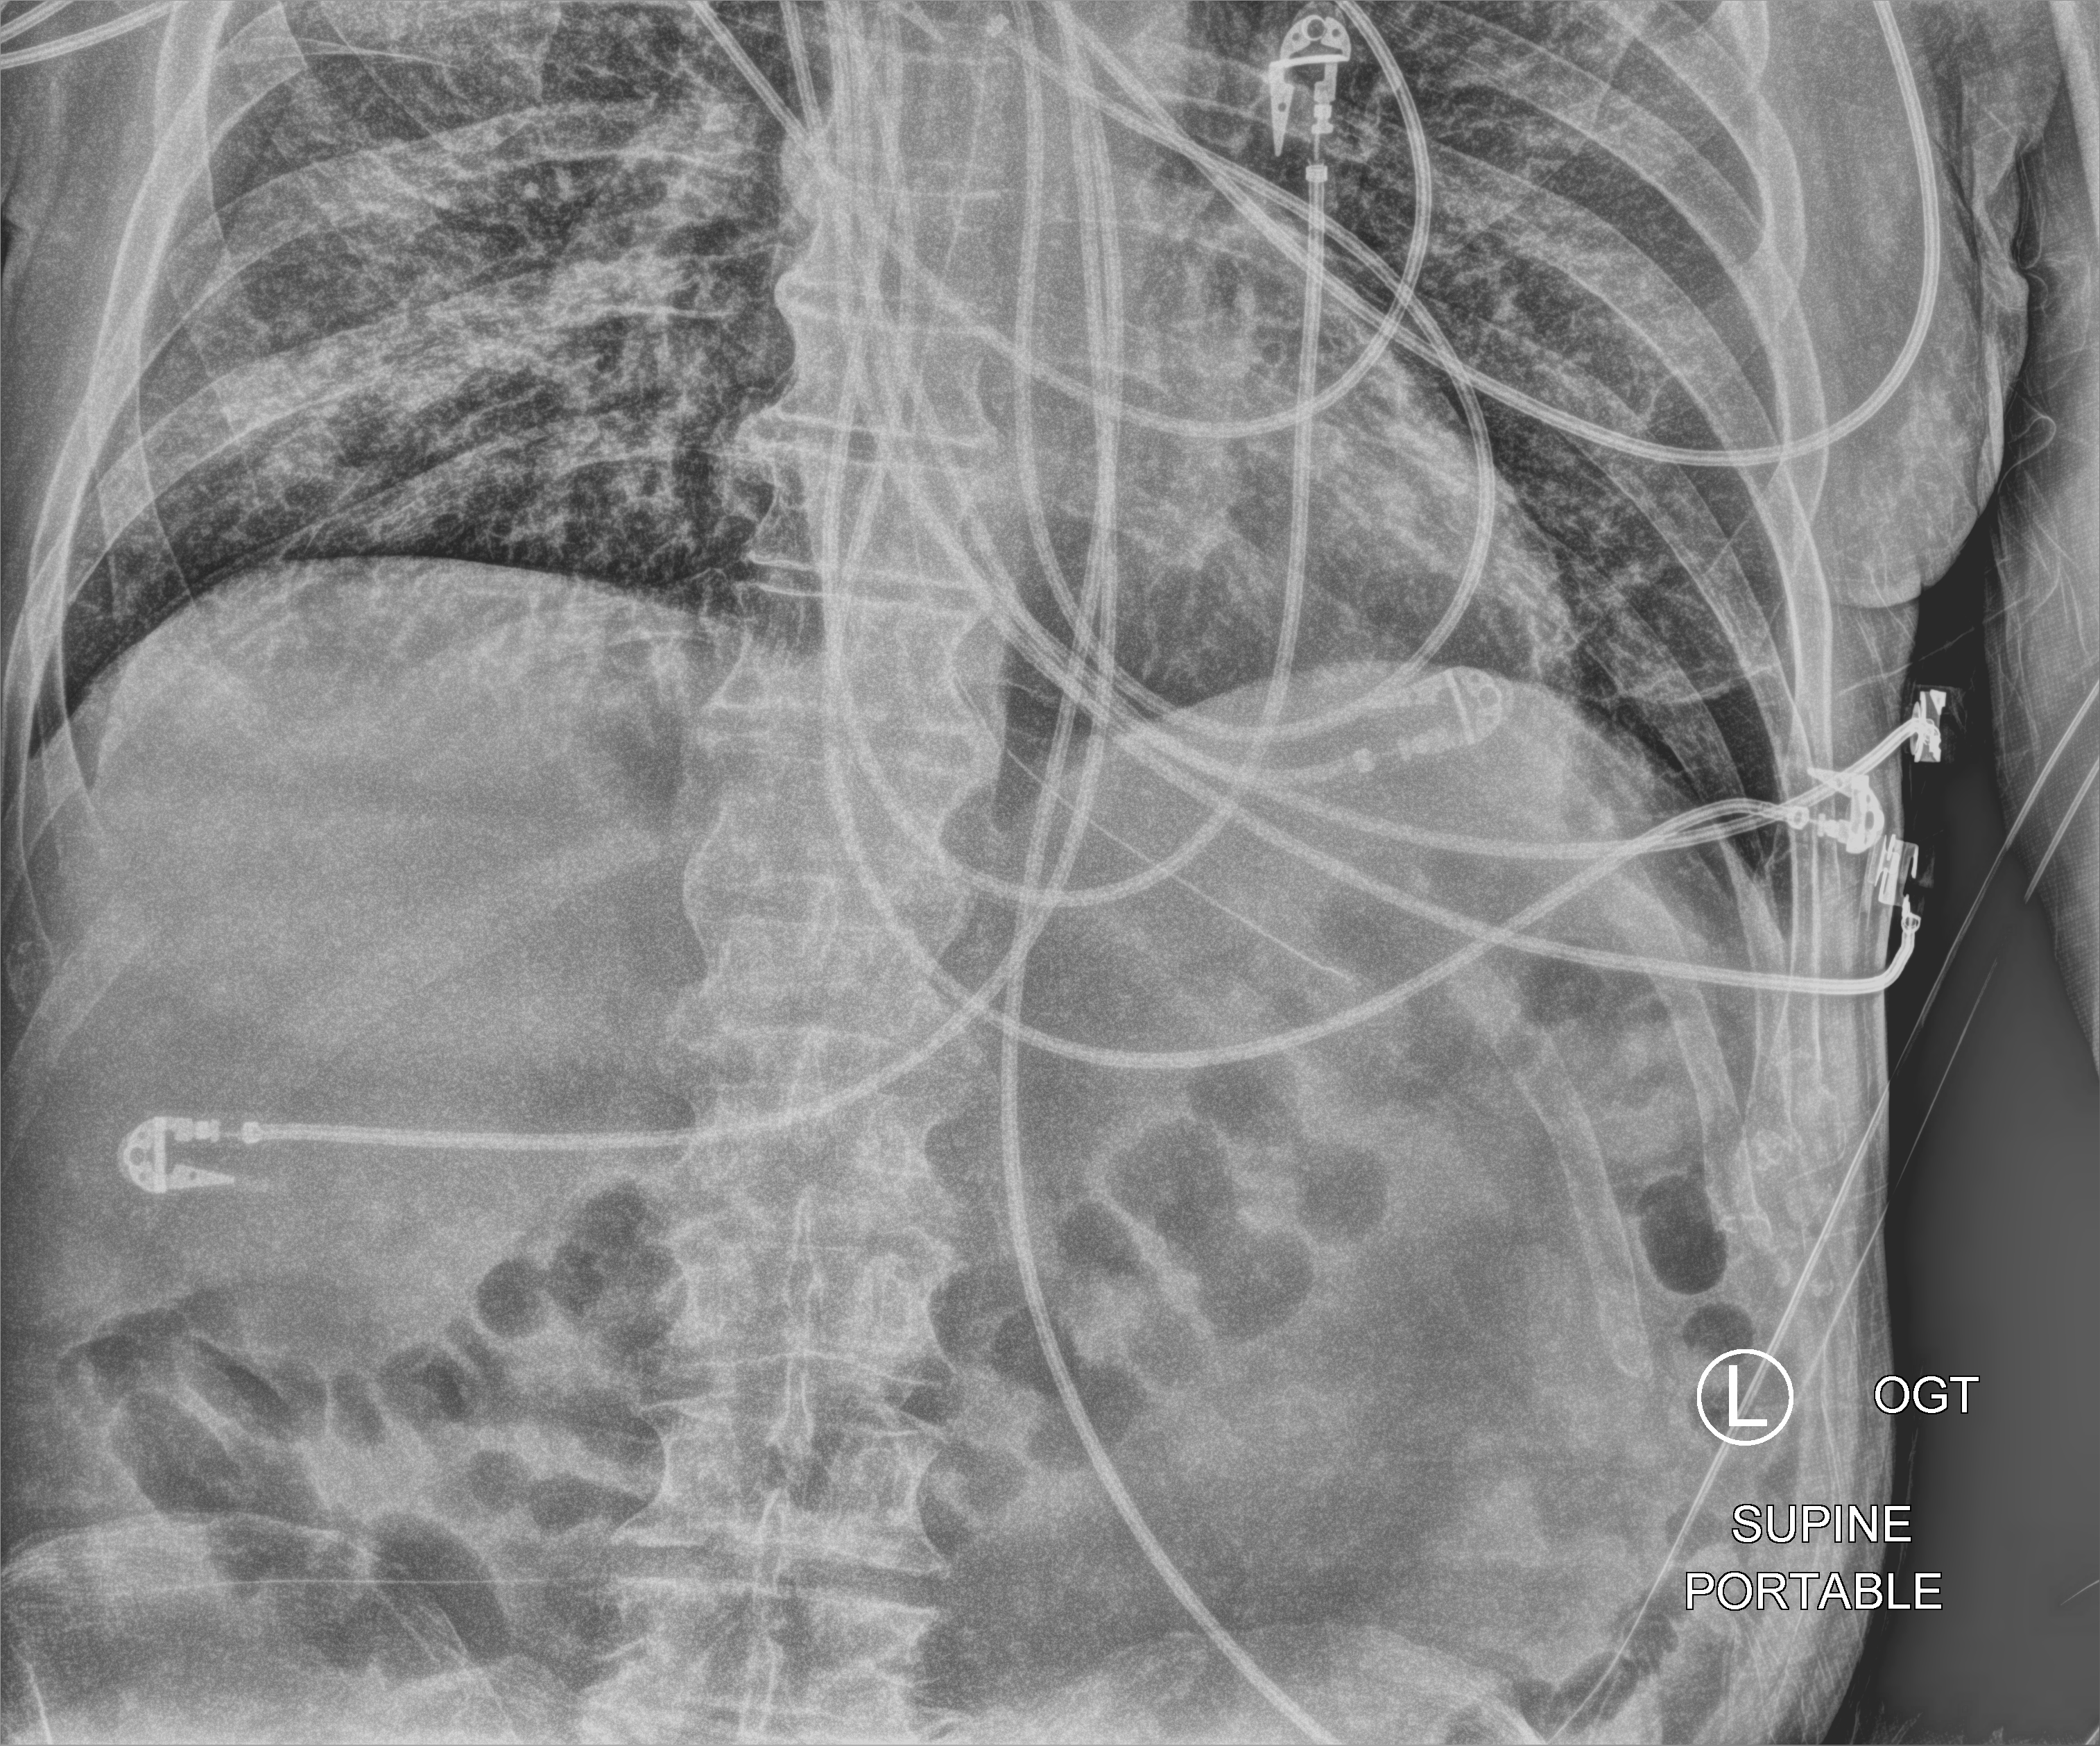
Chest X-ray (portable). Male patient hospitalised with COVID-19, age 60–74 years.
Admission-level facts for this patient (not findings on this image; timing relative to this image not recorded):
- admitted to intensive care during this hospital stay: yes
- other chronic lung disease (admission record): no
- mechanically ventilated during this hospital stay: yes